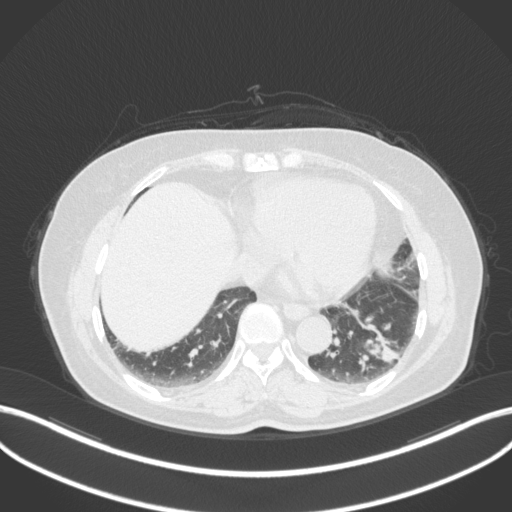
Chest CT, one axial slice; slice 119 of 307 in the series (ordered by position); reconstruction kernel B31f; lung window (W 1500 / L -600 HU); 512 × 512 image matrix, field of view 400 × 400 mm. Patient: female, 59 years. Case-level facts recorded for this patient, not image findings: clinical TNM (as recorded): T2a N0 M0.
Outlined on this slice (rectangle marked by the reading radiologist):
- lung tumour (recorded histology: adenocarcinoma): bounding box (x1, y1, x2, y2) in pixels: (358, 316, 409, 373)